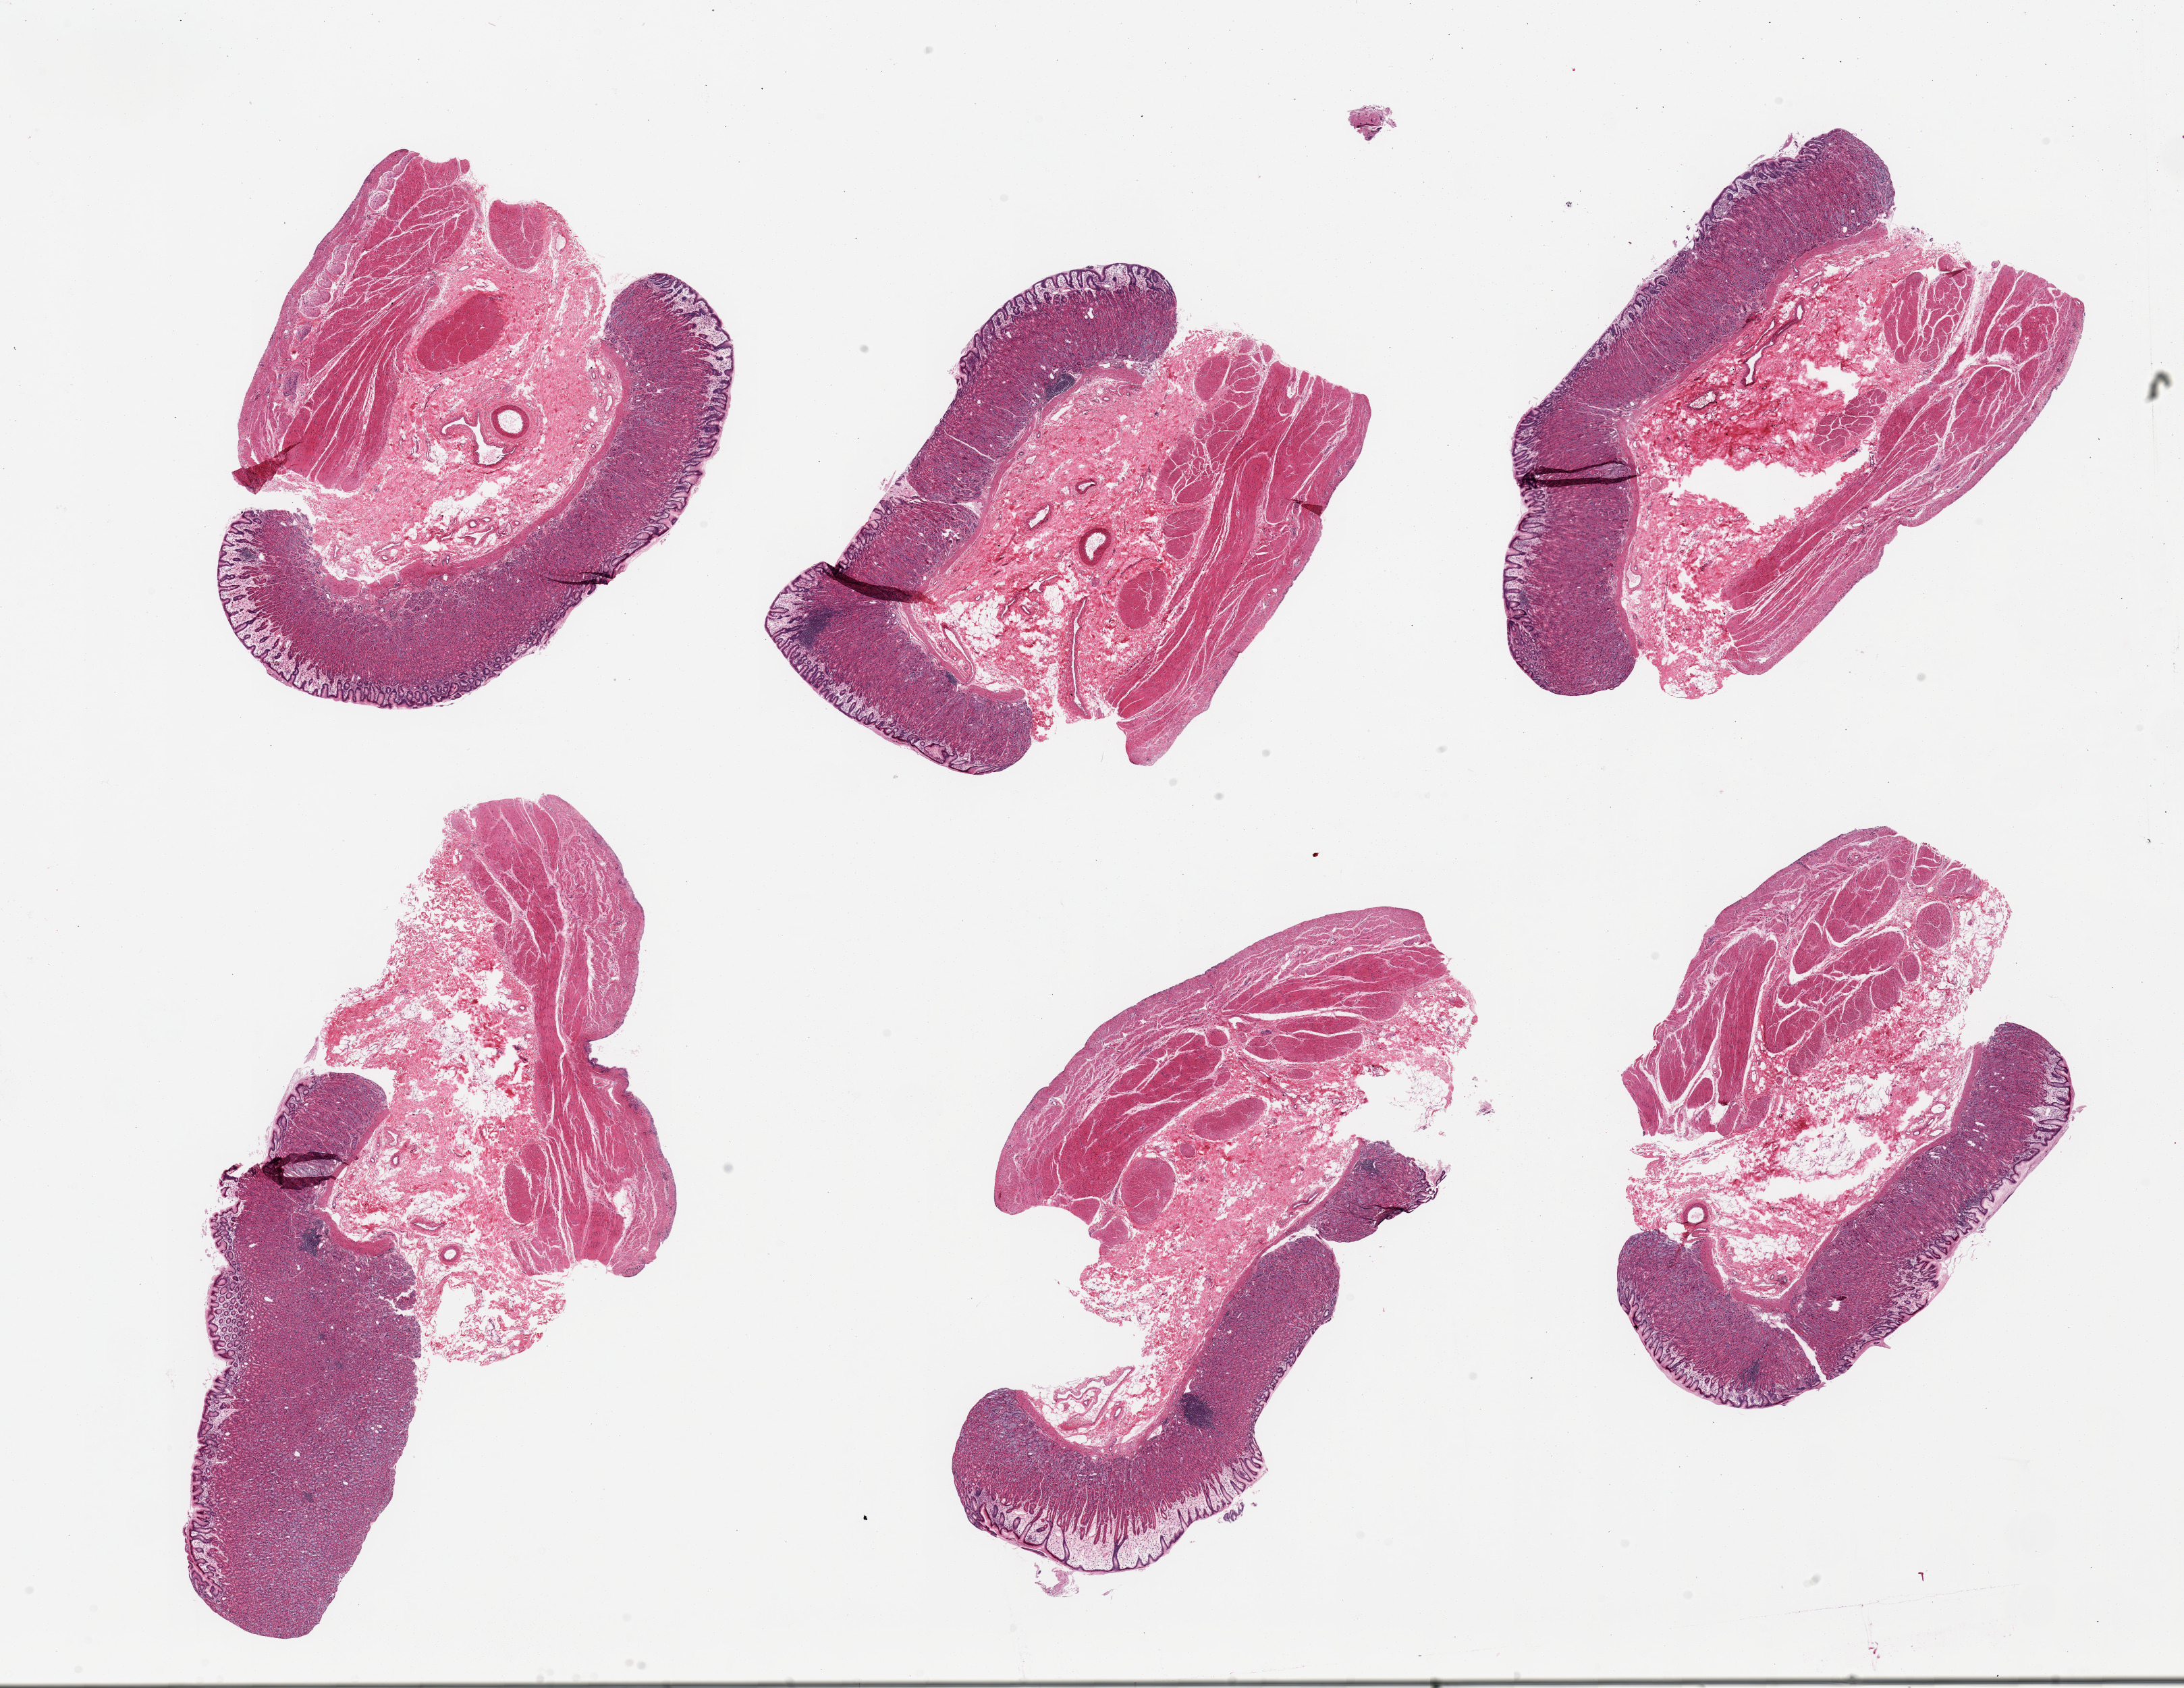
Hematoxylin and eosin (H&E) whole-slide image, shown as a low-resolution overview of the whole scanned area (about 25.6 x 19.8 mm, acquisition: 20x scan); PAXgene-fixed, paraffin-embedded tissue; section of stomach (target tissue); tissue donor sample. Donor: male.
Pathologist's review note for this sample: 6 pieces; full thickness with edema and focal chronic inflammation.